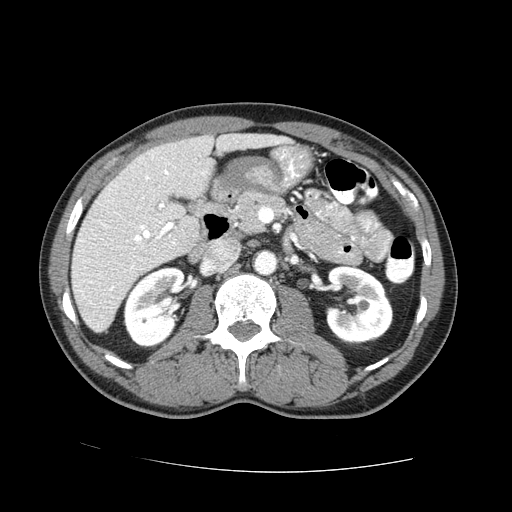
Contrast-enhanced abdominal CT (liver protocol), one axial slice; slice 30 of 73 in the series (ordered by position); 100 kVp; one of 2 acquisitions stored at this slice position; soft-tissue window (W 400 / L 40 HU); 2.5 mm slice thickness; 512 × 512 image matrix. Case-level facts recorded for this patient, not image findings: diagnosis: hepatocellular carcinoma (patient treated with transarterial chemoembolisation; whether this scan precedes or follows treatment is not stated here); TNM stage (as recorded): Stage-IVA; Child-Pugh class: A; tumour differentiation: no biopsy; tumour nodularity: uninodular.
Annotated regions visible in this slice (semi-automatically segmented with operator editing):
- liver parenchyma outside the tumour (the mass and vessels are separate outlines, so this box may not span the whole liver): bounding box (x1, y1, x2, y2) in pixels: (70, 134, 284, 332)
- liver vessels: (90, 170, 173, 291)